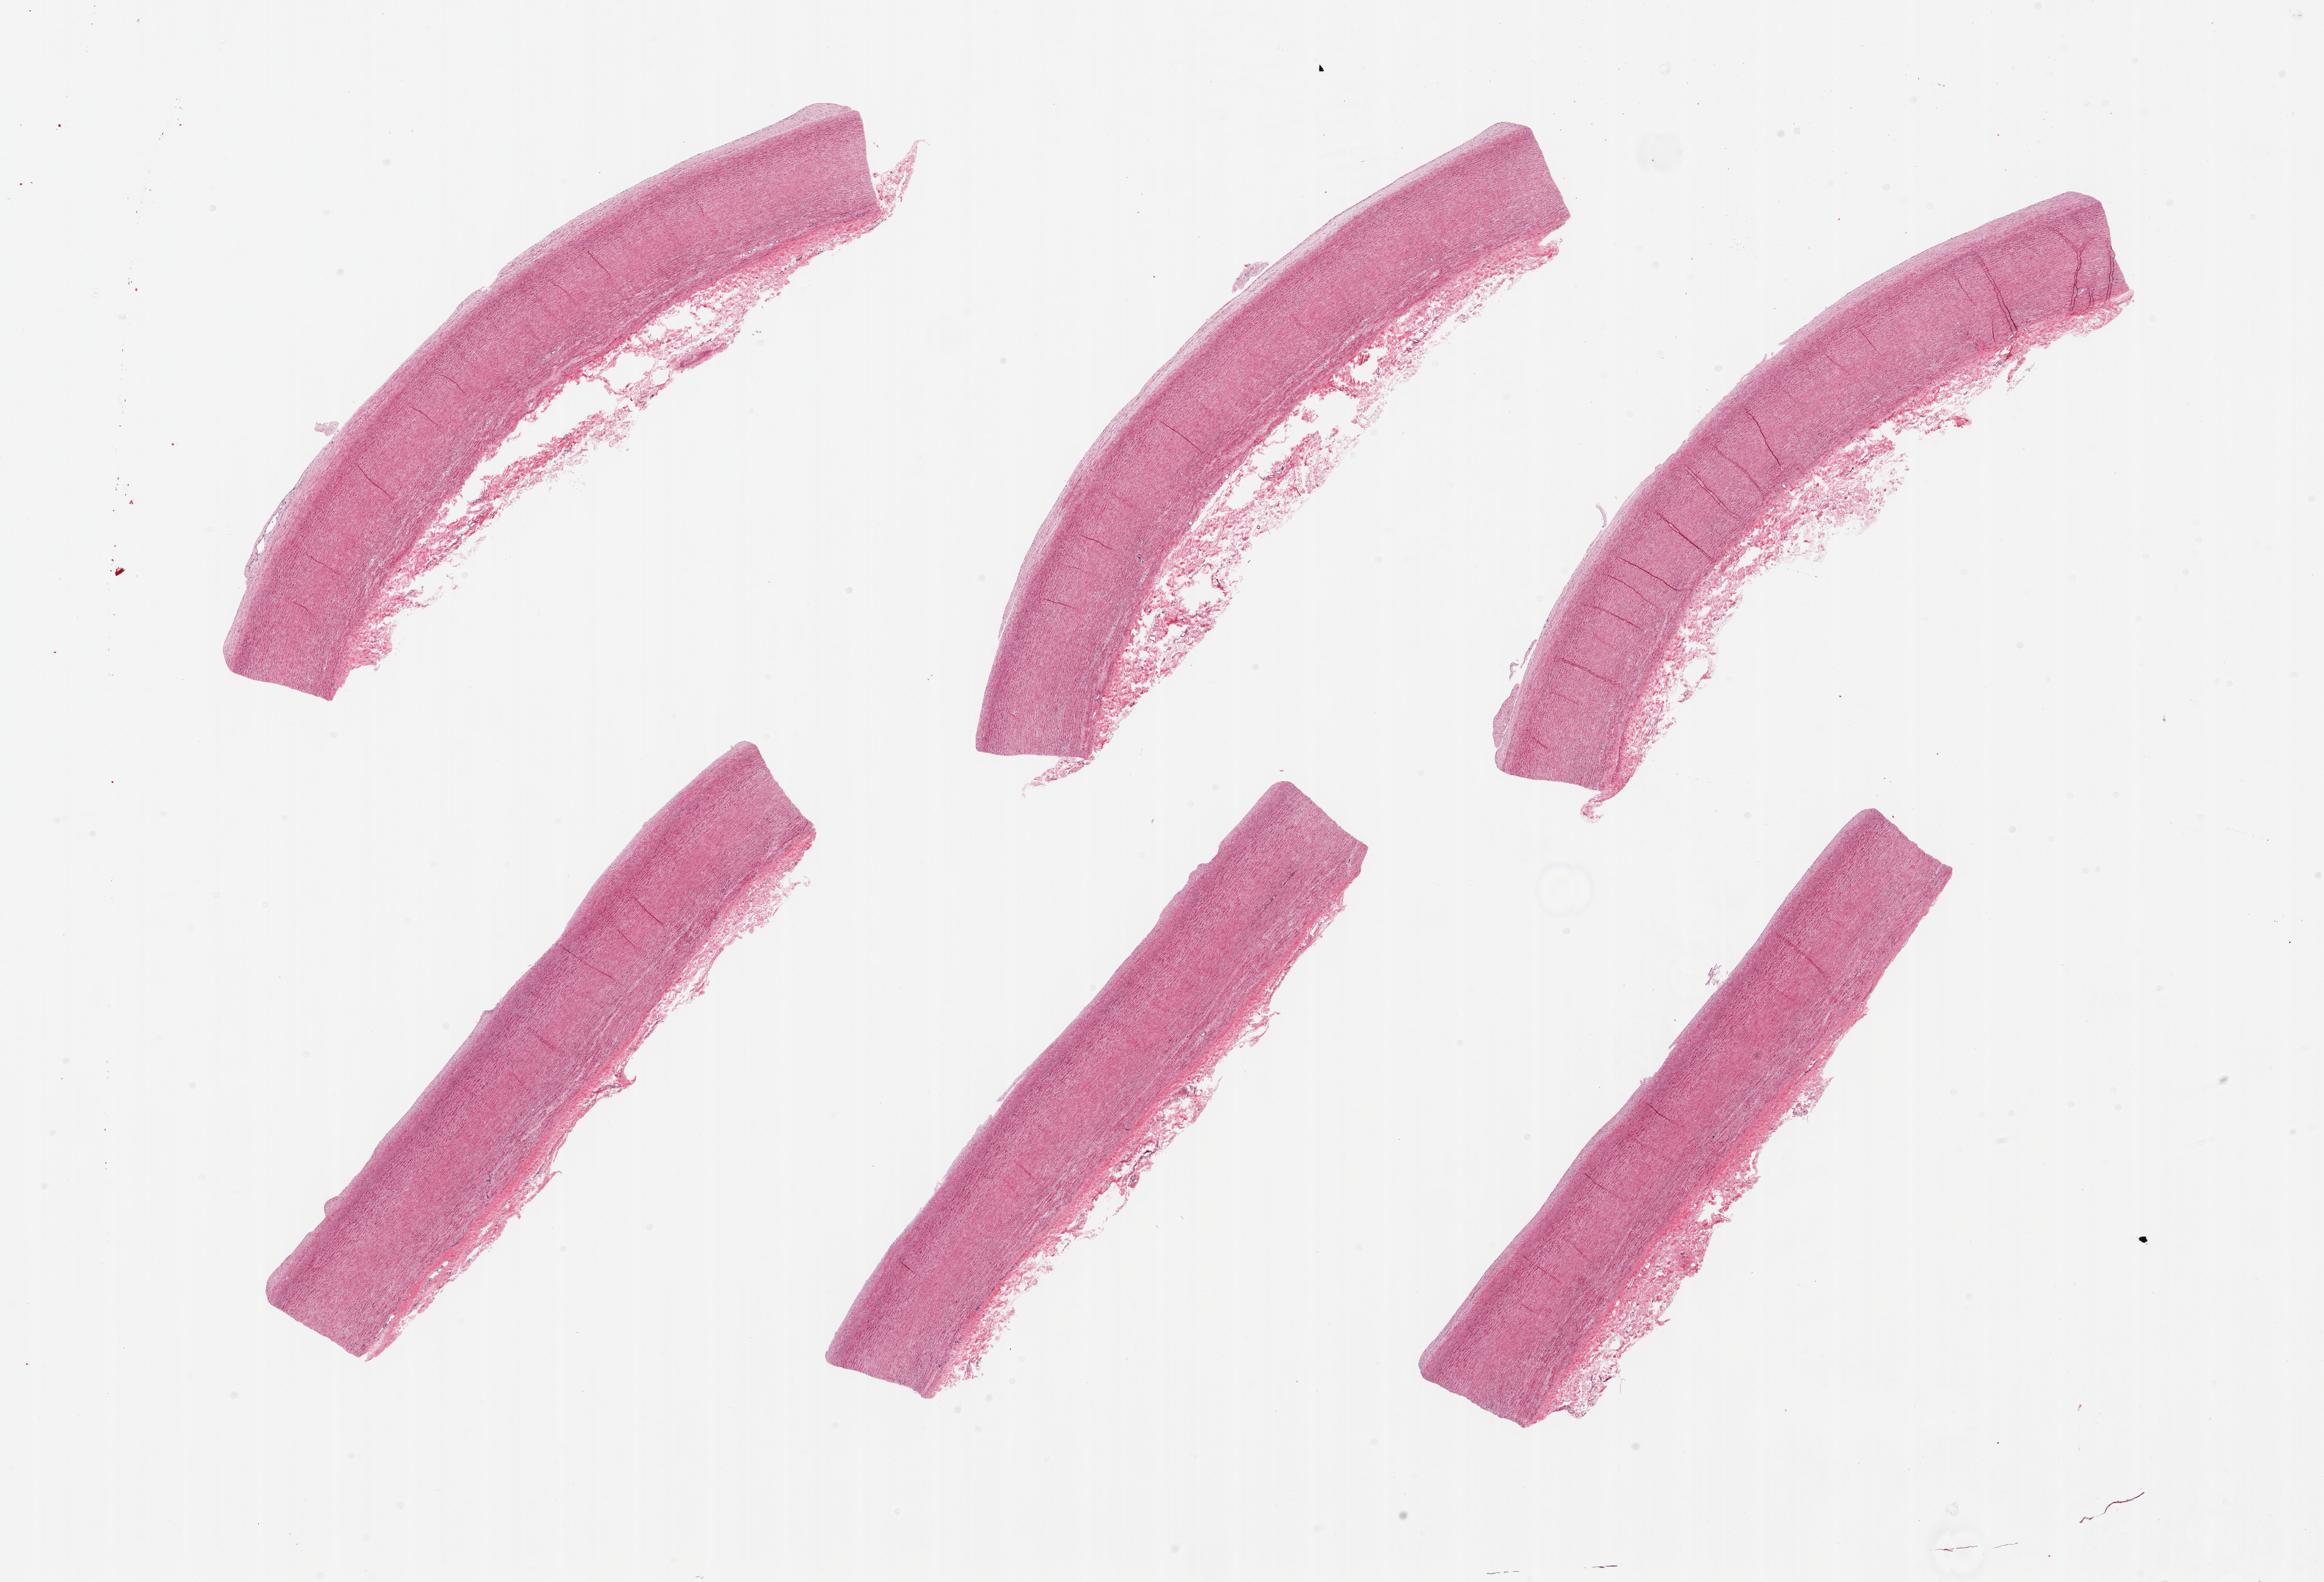
Whole-slide image, H&E stain, brightfield — low-resolution overview of the scanned area, about 30.5 x 20.8 mm; PAXgene-fixed, paraffin-embedded tissue; section of aorta (target tissue); tissue donor sample. Donor sex: male.
Reviewer comment on this tissue sample: 6 pieces, minimal atherosis.